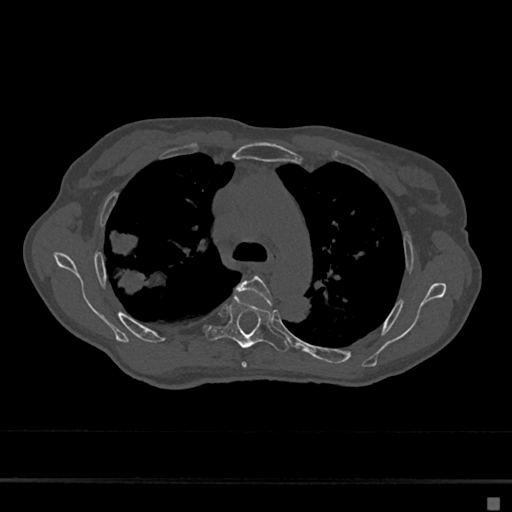
CT including the spine, one axial slice; reconstruction kernel Br40s/3; bone window (W 1800 / L 400 HU); 0.5 mm slice thickness; 512 × 512 image matrix, field of view 360 × 360 mm. Female patient, age 68 years. From the clinical record (not read from this slice): primary cancer: renal.
Annotated regions visible in this slice (semi-automatically segmented with operator editing):
- T4 vertebra: bounding box [x1, y1, x2, y2] px = [236, 276, 273, 368]
- T5 vertebra: [207, 296, 288, 352]